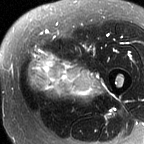
MRI of an extremity soft-tissue mass, one axial slice. Position 21 of 60 along the scan axis. T2-weighted fat-saturated. MR volume resampled by the dataset authors to the PET/CT grid (not the native acquisition matrix). 3.27 mm slice thickness. 144 × 144 image matrix, field of view 141 × 141 mm. Female patient. From the clinical record (not read from this slice): histological type: pleiomorphic leiomyosarcoma; grade: intermediate; site of the primary tumour: left thigh.
Annotated regions visible in this slice (expert contour drawn on MRI and transferred to this co-registered scan by the dataset authors):
- gross tumour volume including surrounding oedema: bounding box (x1, y1, x2, y2) in pixels: (25, 49, 106, 100)
- gross tumour volume (mass): (27, 51, 94, 100)